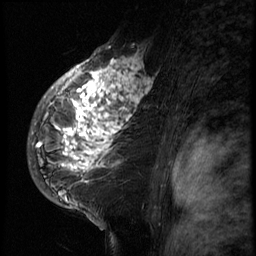
Breast MRI (dynamic contrast-enhanced), one sagittal slice. Position 47 of 66 along the scan axis. 3 images stored at this slice position (order not interpretable as contrast timing). 1.5 T. TE 4.2 ms, TR 8.9 ms. 2.5 mm slice thickness. 256 × 256 image matrix. Female patient, age 39 years. Case-level facts recorded for this patient, not image findings: setting: breast cancer imaged before/during neoadjuvant chemotherapy; receptor status: HER2-positive.
Structures marked on this image (semi-automatic segmentation, software-assisted and operator-edited):
- analysis volume of interest (the breast-tissue region the enhancement analysis was run in; not a lesion): bounding box (x1, y1, x2, y2) in pixels: (29, 44, 166, 196)
- tumour enhancement mask (voxels above the 140 % enhancement threshold inside the analysis volume of interest): (35, 46, 153, 171)